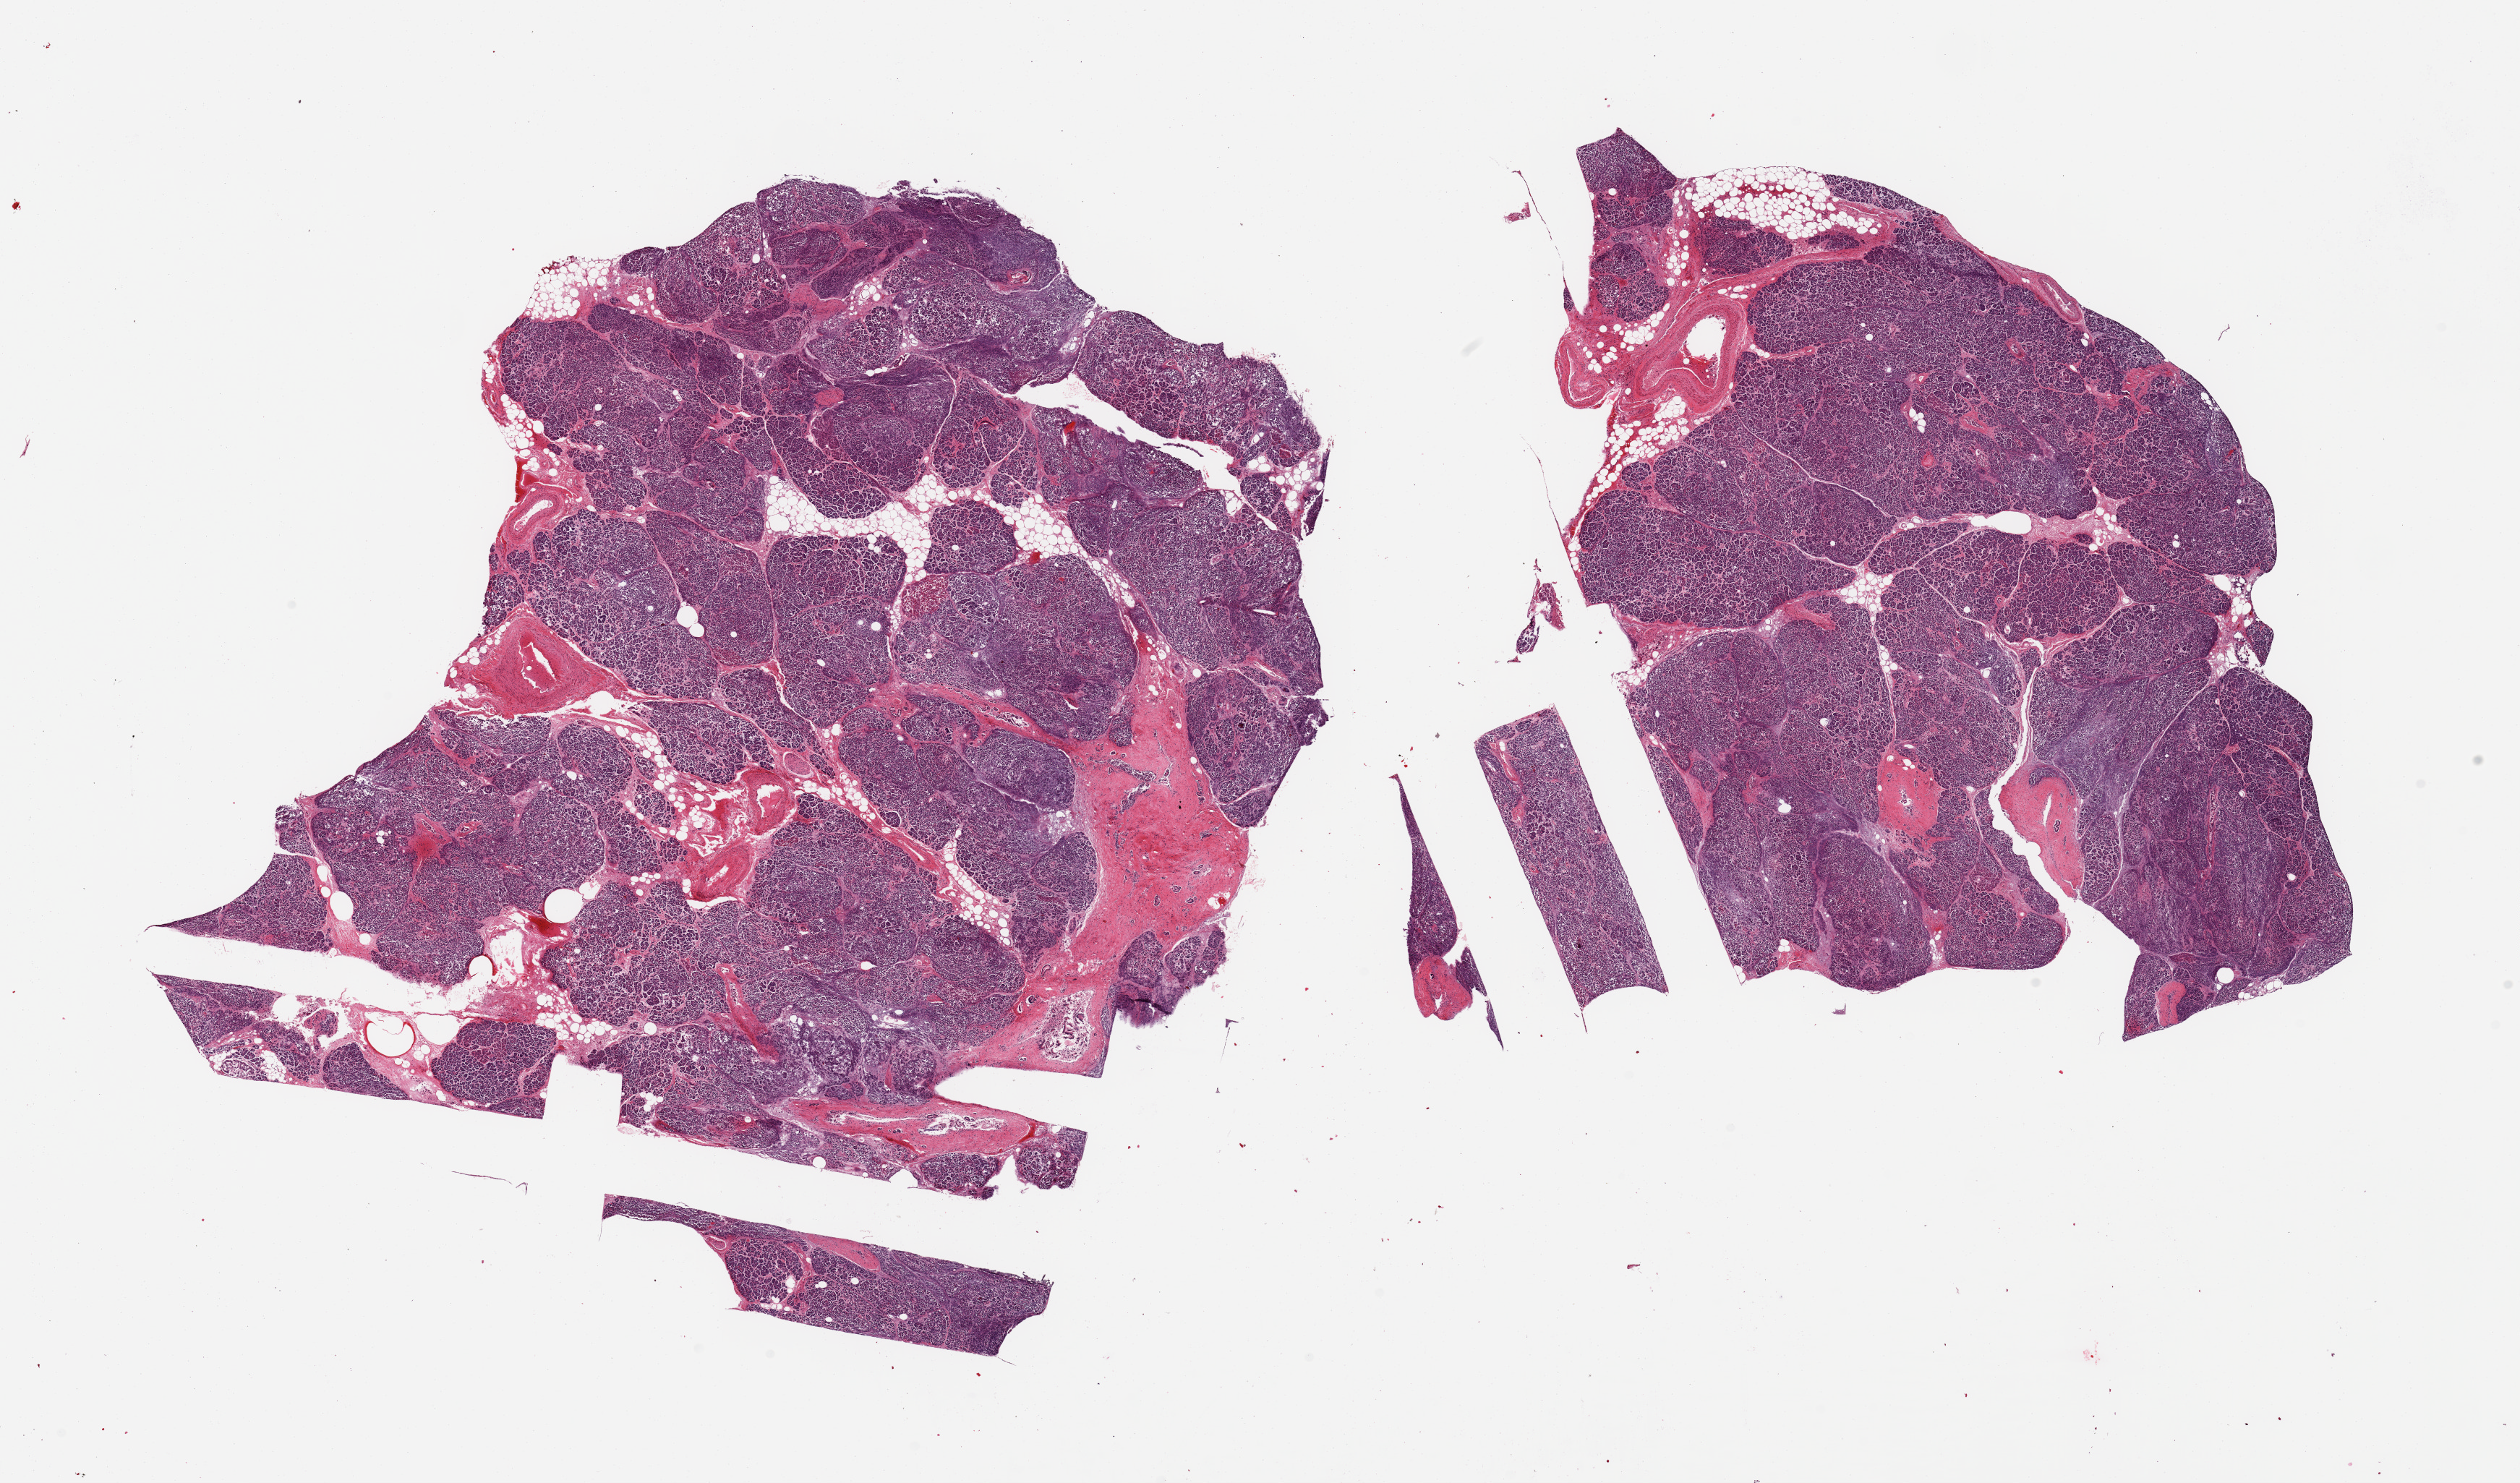
H&E whole-slide image, low-resolution overview of the scanned area, about 27.6 x 16.2 mm (slide scanned at 20x); PAXgene-fixed paraffin-embedded (PFPE) section; target tissue: pancreas; tissue donor sample. Donor sex: male.
Pathologist's review note for this sample: 2 pieces; periductal and interstitial fibrosis with parenchymal autolysis; rare islets of Langerhans.